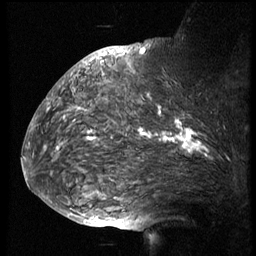
Breast MRI (dynamic contrast-enhanced), one sagittal slice; slice 46 of 74 in the series (ordered by position); 3 images stored at this slice position (order not interpretable as contrast timing); 1.5 T; TE 4.2 ms, TR 8.9 ms; 2.5 mm slice thickness; 256 × 256 image matrix. Female patient, age 57 years. Case-level facts recorded for this patient, not image findings: setting: breast cancer imaged before/during neoadjuvant chemotherapy; receptor status: HER2-positive.
Annotated regions visible in this slice (semi-automatic segmentation, software-assisted and operator-edited):
- analysis volume of interest (the breast-tissue region the enhancement analysis was run in; not a lesion): bounding box <51,67,246,173> (left, top, right, bottom; pixels)
- tumour enhancement mask (voxels above the 140 % enhancement threshold inside the analysis volume of interest): <57,108,207,153>